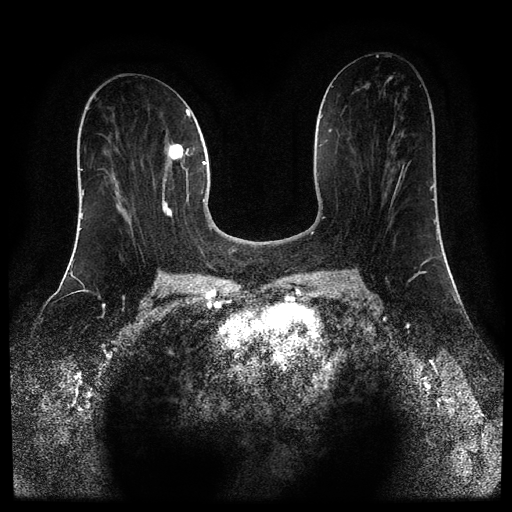
Breast MRI (dynamic contrast-enhanced, multi-phase), one axial slice; slice 41 of 110 in the series (ordered by position); dynamic contrast-enhanced series, time point 2 of 5 at this slice position (early post-contrast); 1.5 T; TE 2.6 ms, TR 5.4 ms; 2 mm slice thickness; 512 × 512 image matrix. Female patient, age 43 years.
Outlined on this slice (semi-automatically segmented with operator editing):
- breast lesion (labelled 'tumour' in the annotation; benign lesions carry a separate 'benign' label): bounding box <162,143,184,218> (left, top, right, bottom; pixels)